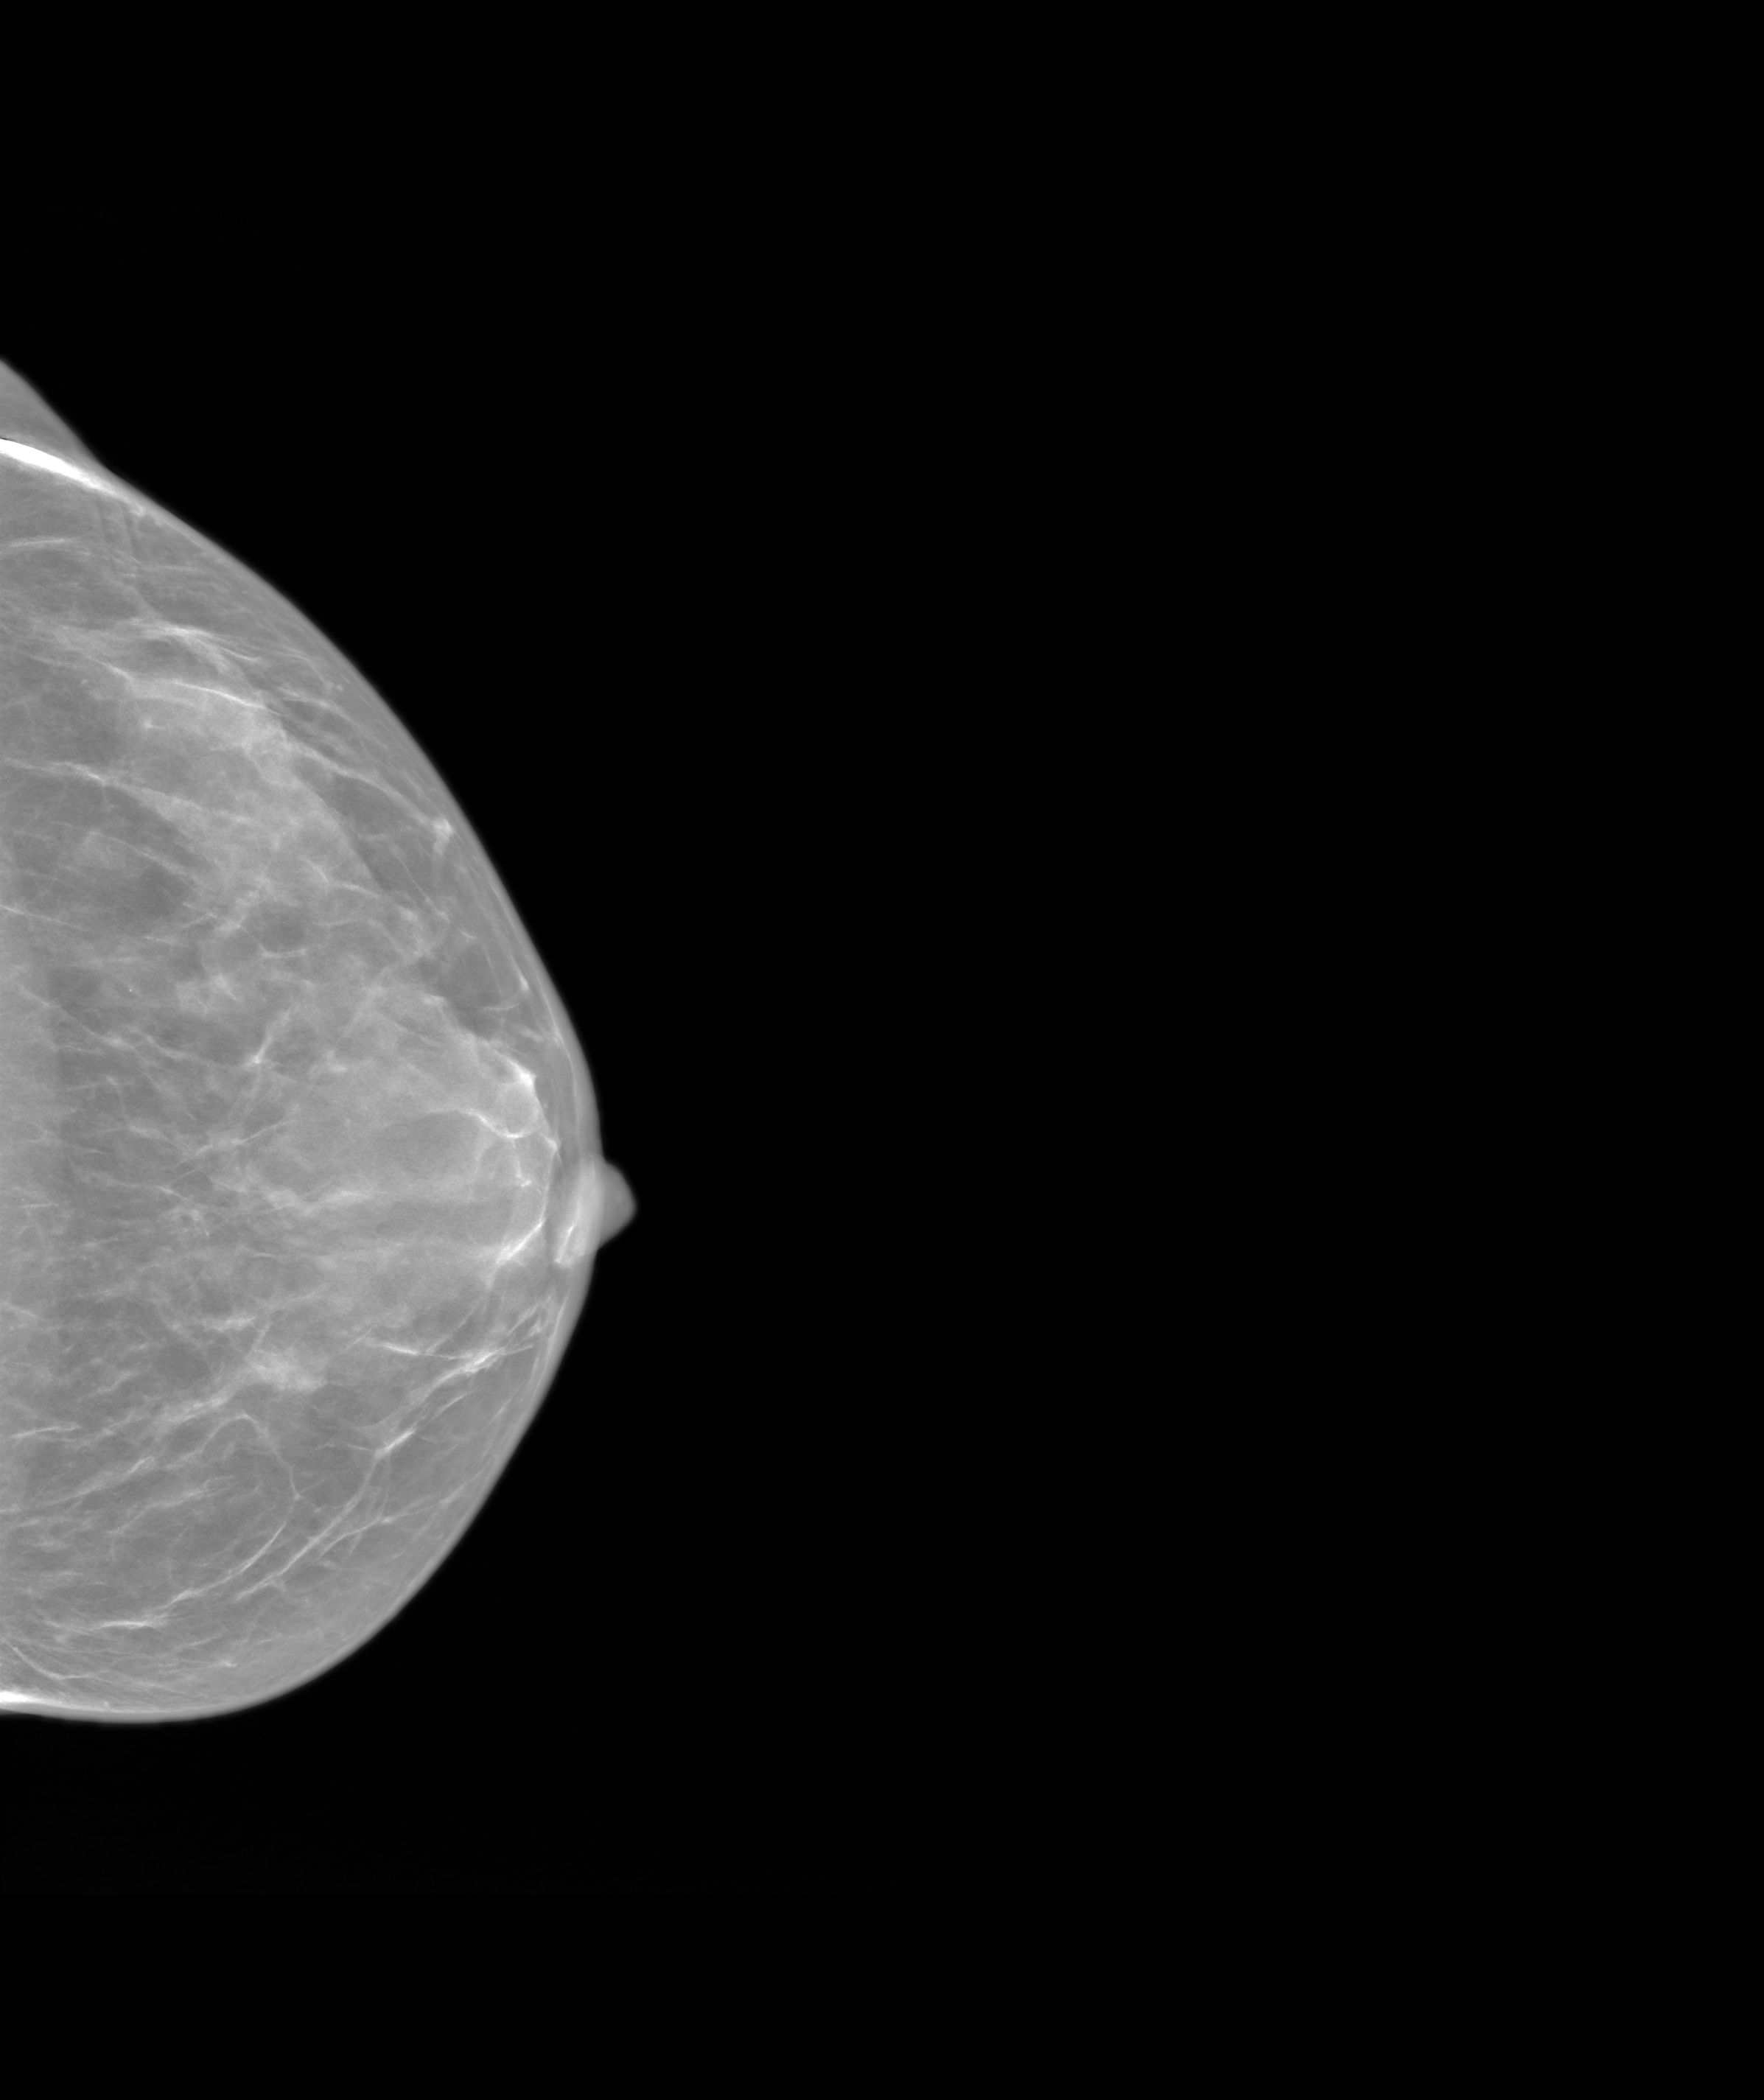
Synthesized 2-D mammogram reconstructed from digital breast tomosynthesis, left breast, craniocaudal (CC) view, screening examination, system: SenoIris_1SP1.1(421). Female patient, age 48 years.
Breast density at the screening exam (both breasts): heterogeneously dense (BI-RADS density category c). Final BI-RADS assessment for this screening round (tomosynthesis exam, both breasts): category 2. Recall: no recall after this screen.